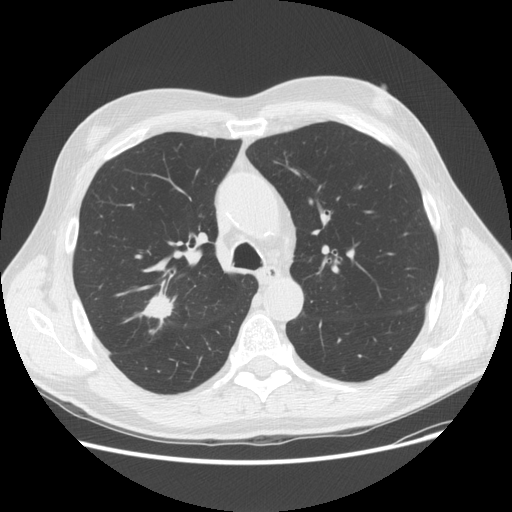
Low-dose screening chest CT, one axial slice. Slice 105 of 156 in the series (ordered by position). 120 kVp. Lung window (W 1500 / L -600 HU). 2.5 mm slice thickness. 512 × 512 image matrix, field of view 380 × 380 mm.
Structures marked on this image (outlined manually by an expert reader):
- lesion 1 (tumor, upper lobe of right lung): box from (x=142, y=287) to (x=176, y=334) px